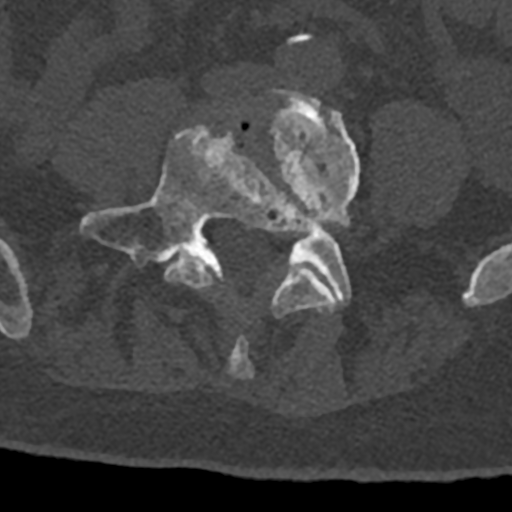
CT including the spine, one axial slice. Position 224 of 797 along the scan axis. Bone window (W 1800 / L 400 HU). 0.5 mm slice thickness. 512 × 512 image matrix, field of view 160 × 160 mm. Male patient, age 74 years. From the clinical record (not read from this slice): primary cancer: renal; vertebrae with lytic lesions (as recorded): T10, L1, L2, L3, L4, L5.
Outlined on this slice (semi-automatically segmented with operator editing):
- L4 vertebra: bounding box [x1, y1, x2, y2] px = [164, 90, 360, 378]
- L5 vertebra: [80, 126, 351, 305]